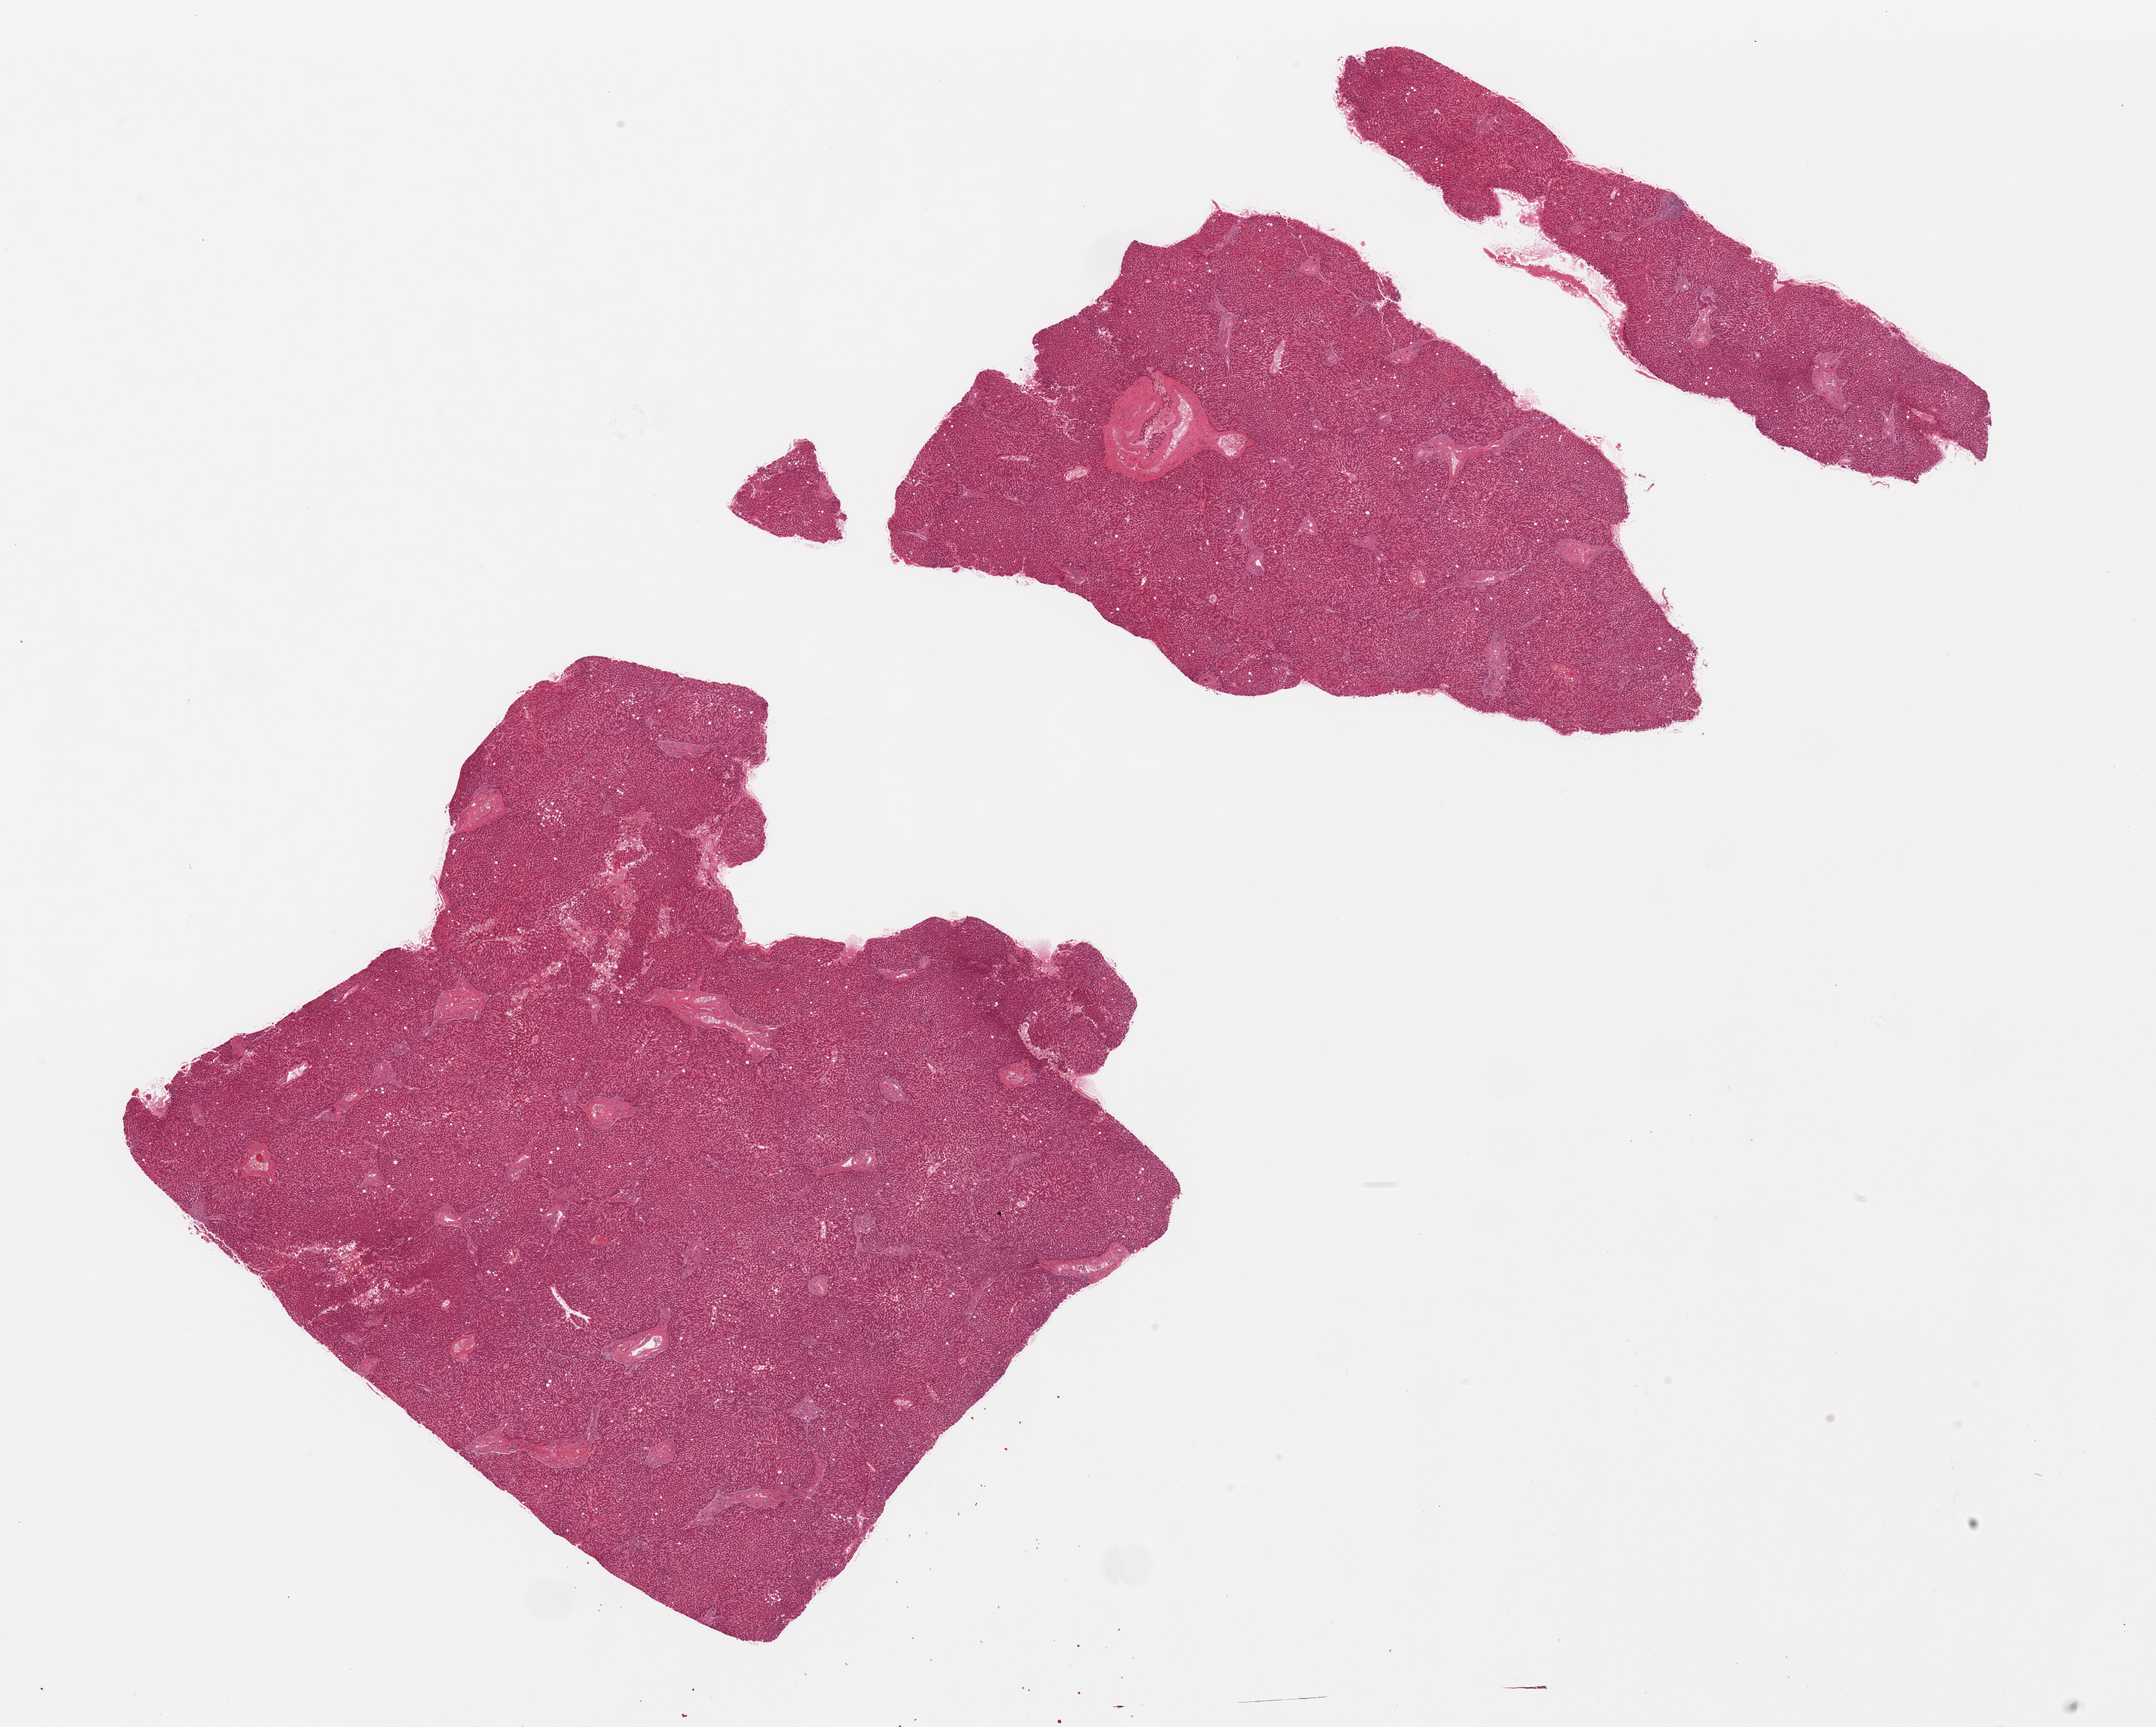
Whole-slide image, hematoxylin and eosin (H&E) stain, brightfield, whole scanned area (about 26.6 x 21.3 mm, from a 20x scan) shown as a low-resolution overview; PAXgene-fixed, paraffin-embedded tissue; section of liver (target tissue); donor tissue sample. Donor: male.
Review note (as recorded): 2 fragmented pieces; 5% macrovesicular steatosis.